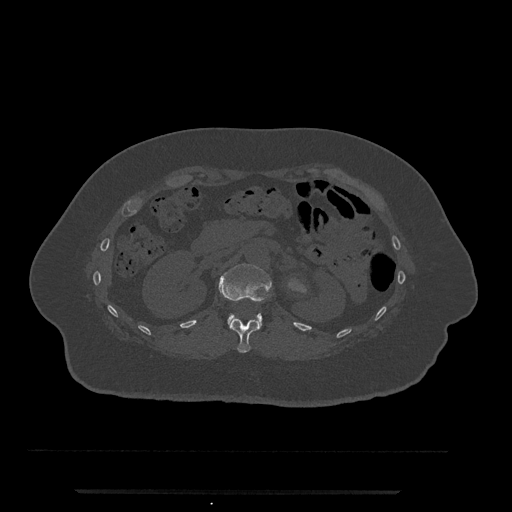
CT including the spine, one axial slice; position 137 of 797 along the scan axis; bone window (W 1800 / L 400 HU); 0.5 mm slice thickness; 512 × 512 image matrix, field of view 440 × 440 mm. Female patient, age 51 years. Case-level facts recorded for this patient, not image findings: primary cancer: neuro.
Structures marked on this image (semi-automatically segmented with operator editing):
- L1 vertebra: bounding box <218,264,271,329> (left, top, right, bottom; pixels)
- T12 vertebra: <230,317,259,353>